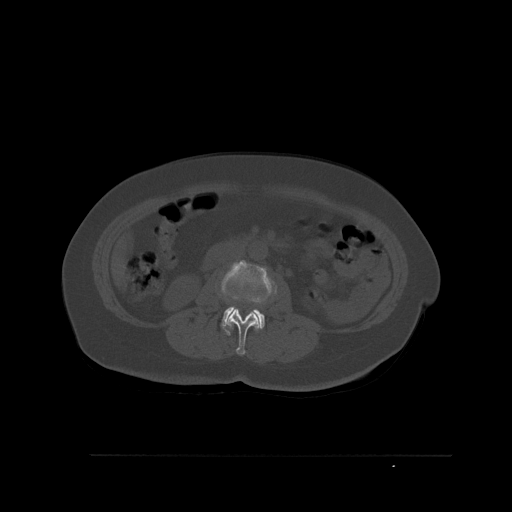
CT including the spine, one axial slice. Position 237 of 527 along the scan axis. Bone window (W 1800 / L 400 HU). 1.5 mm slice thickness. 512 × 512 image matrix. Patient: female, 73 years. Case-level facts recorded for this patient, not image findings: primary cancer: breast.
Outlined on this slice (semi-automatically segmented with operator editing):
- L2 vertebra: bounding box <227,308,259,355> (left, top, right, bottom; pixels)
- L3 vertebra: <221,260,277,336>
- L4 vertebra: <247,311,260,331>